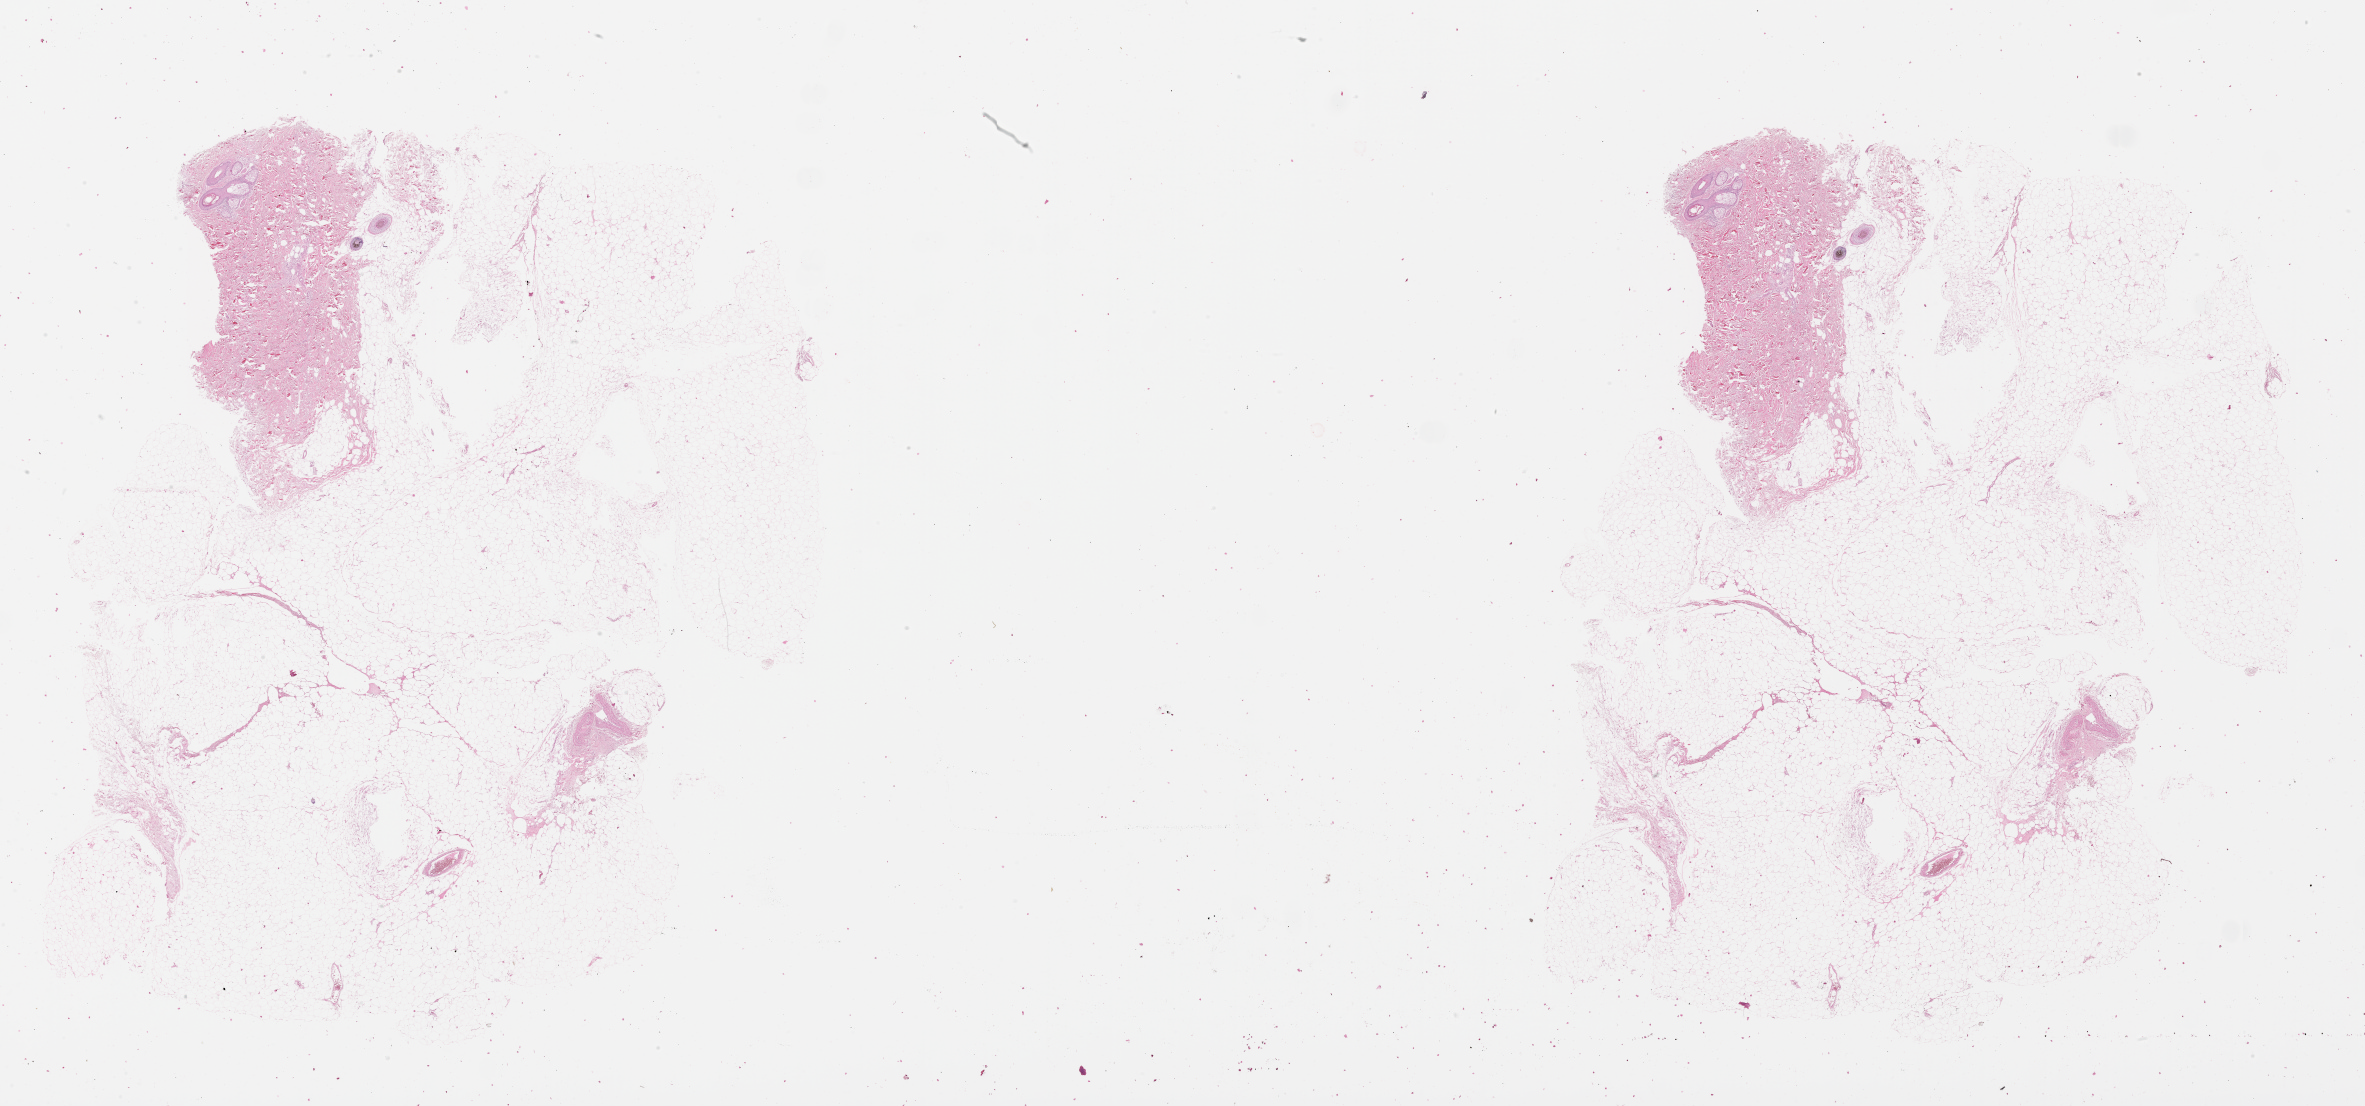
H&E-stained whole-slide image — low-resolution overview of the scanned area, about 38.1 x 17.8 mm (acquisition: 20x scan); normal (non-tumour) tissue sample, sampled site: trunk. Patient: male, age 61 years.
This section: normal (non-tumour) tissue from the same patient. Patient diagnosis: Malignant melanoma, NOS.